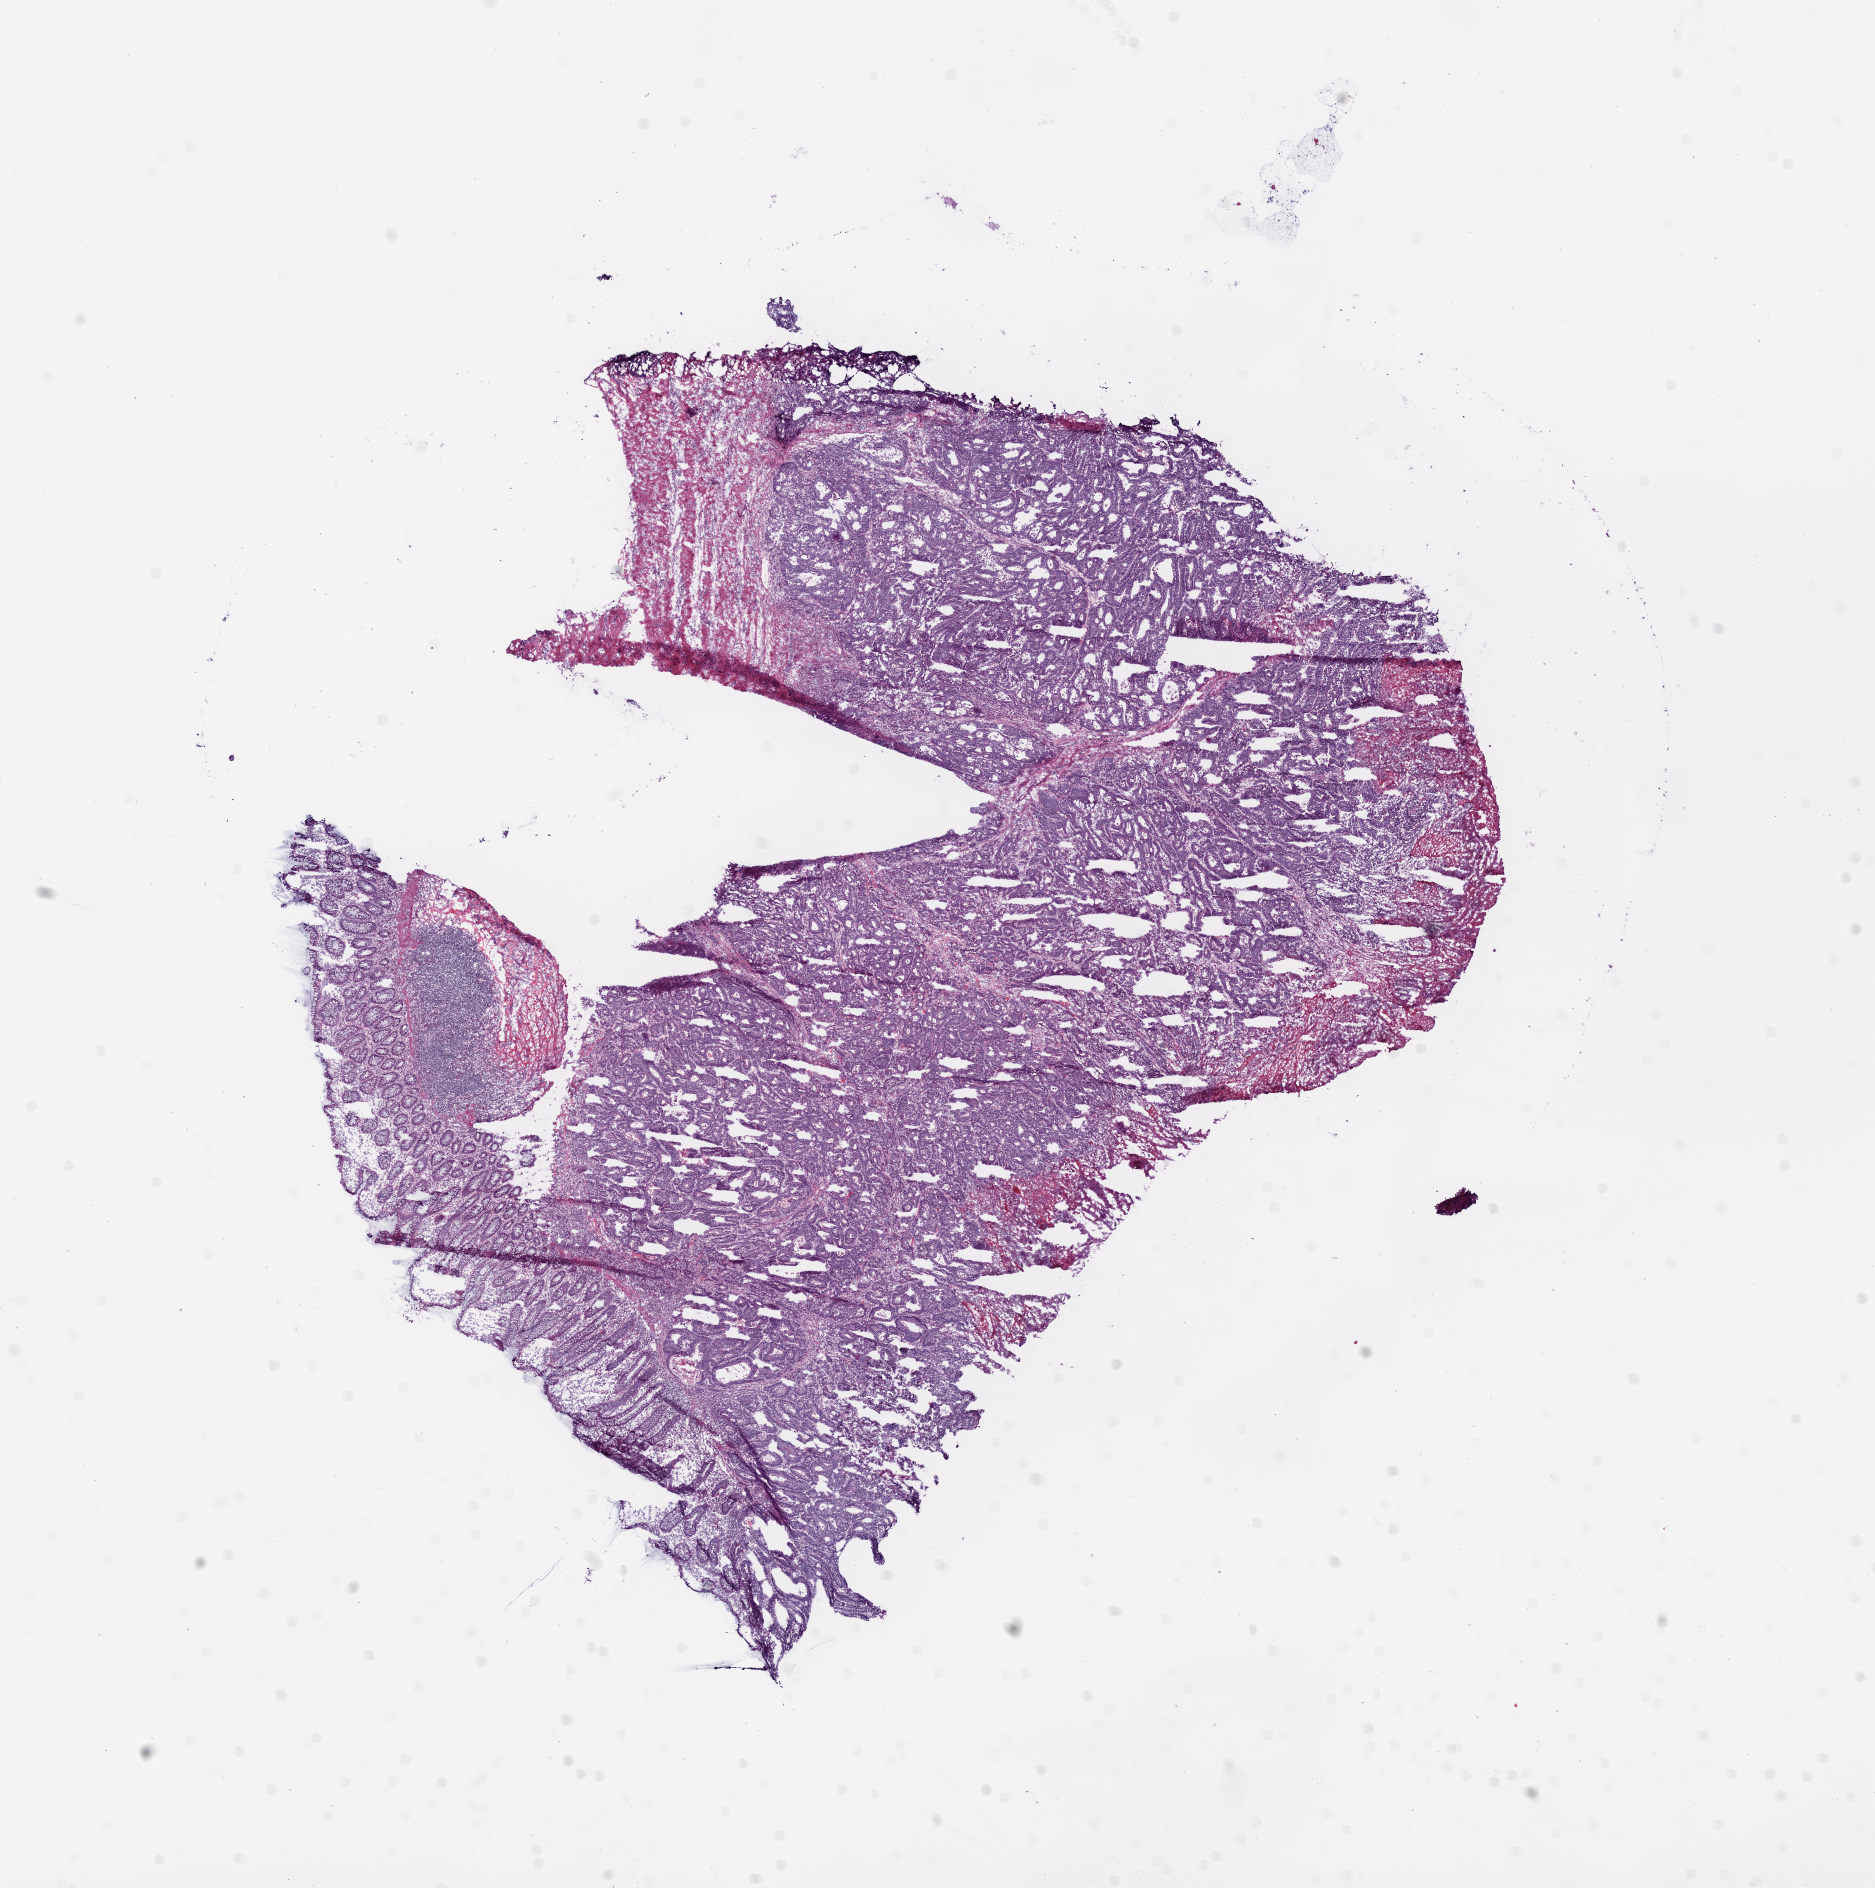
Hematoxylin and eosin (H&E) stained whole-slide image, a low-resolution overview of the entire scanned area, about 15.0 x 15.1 mm (slide scanned at 20x); frozen section from the bottom of the tissue portion; sample: primary tumour, colon. Patient: male, age at initial diagnosis 70 years.
Diagnosis: Adenocarcinoma, NOS (ascending colon).